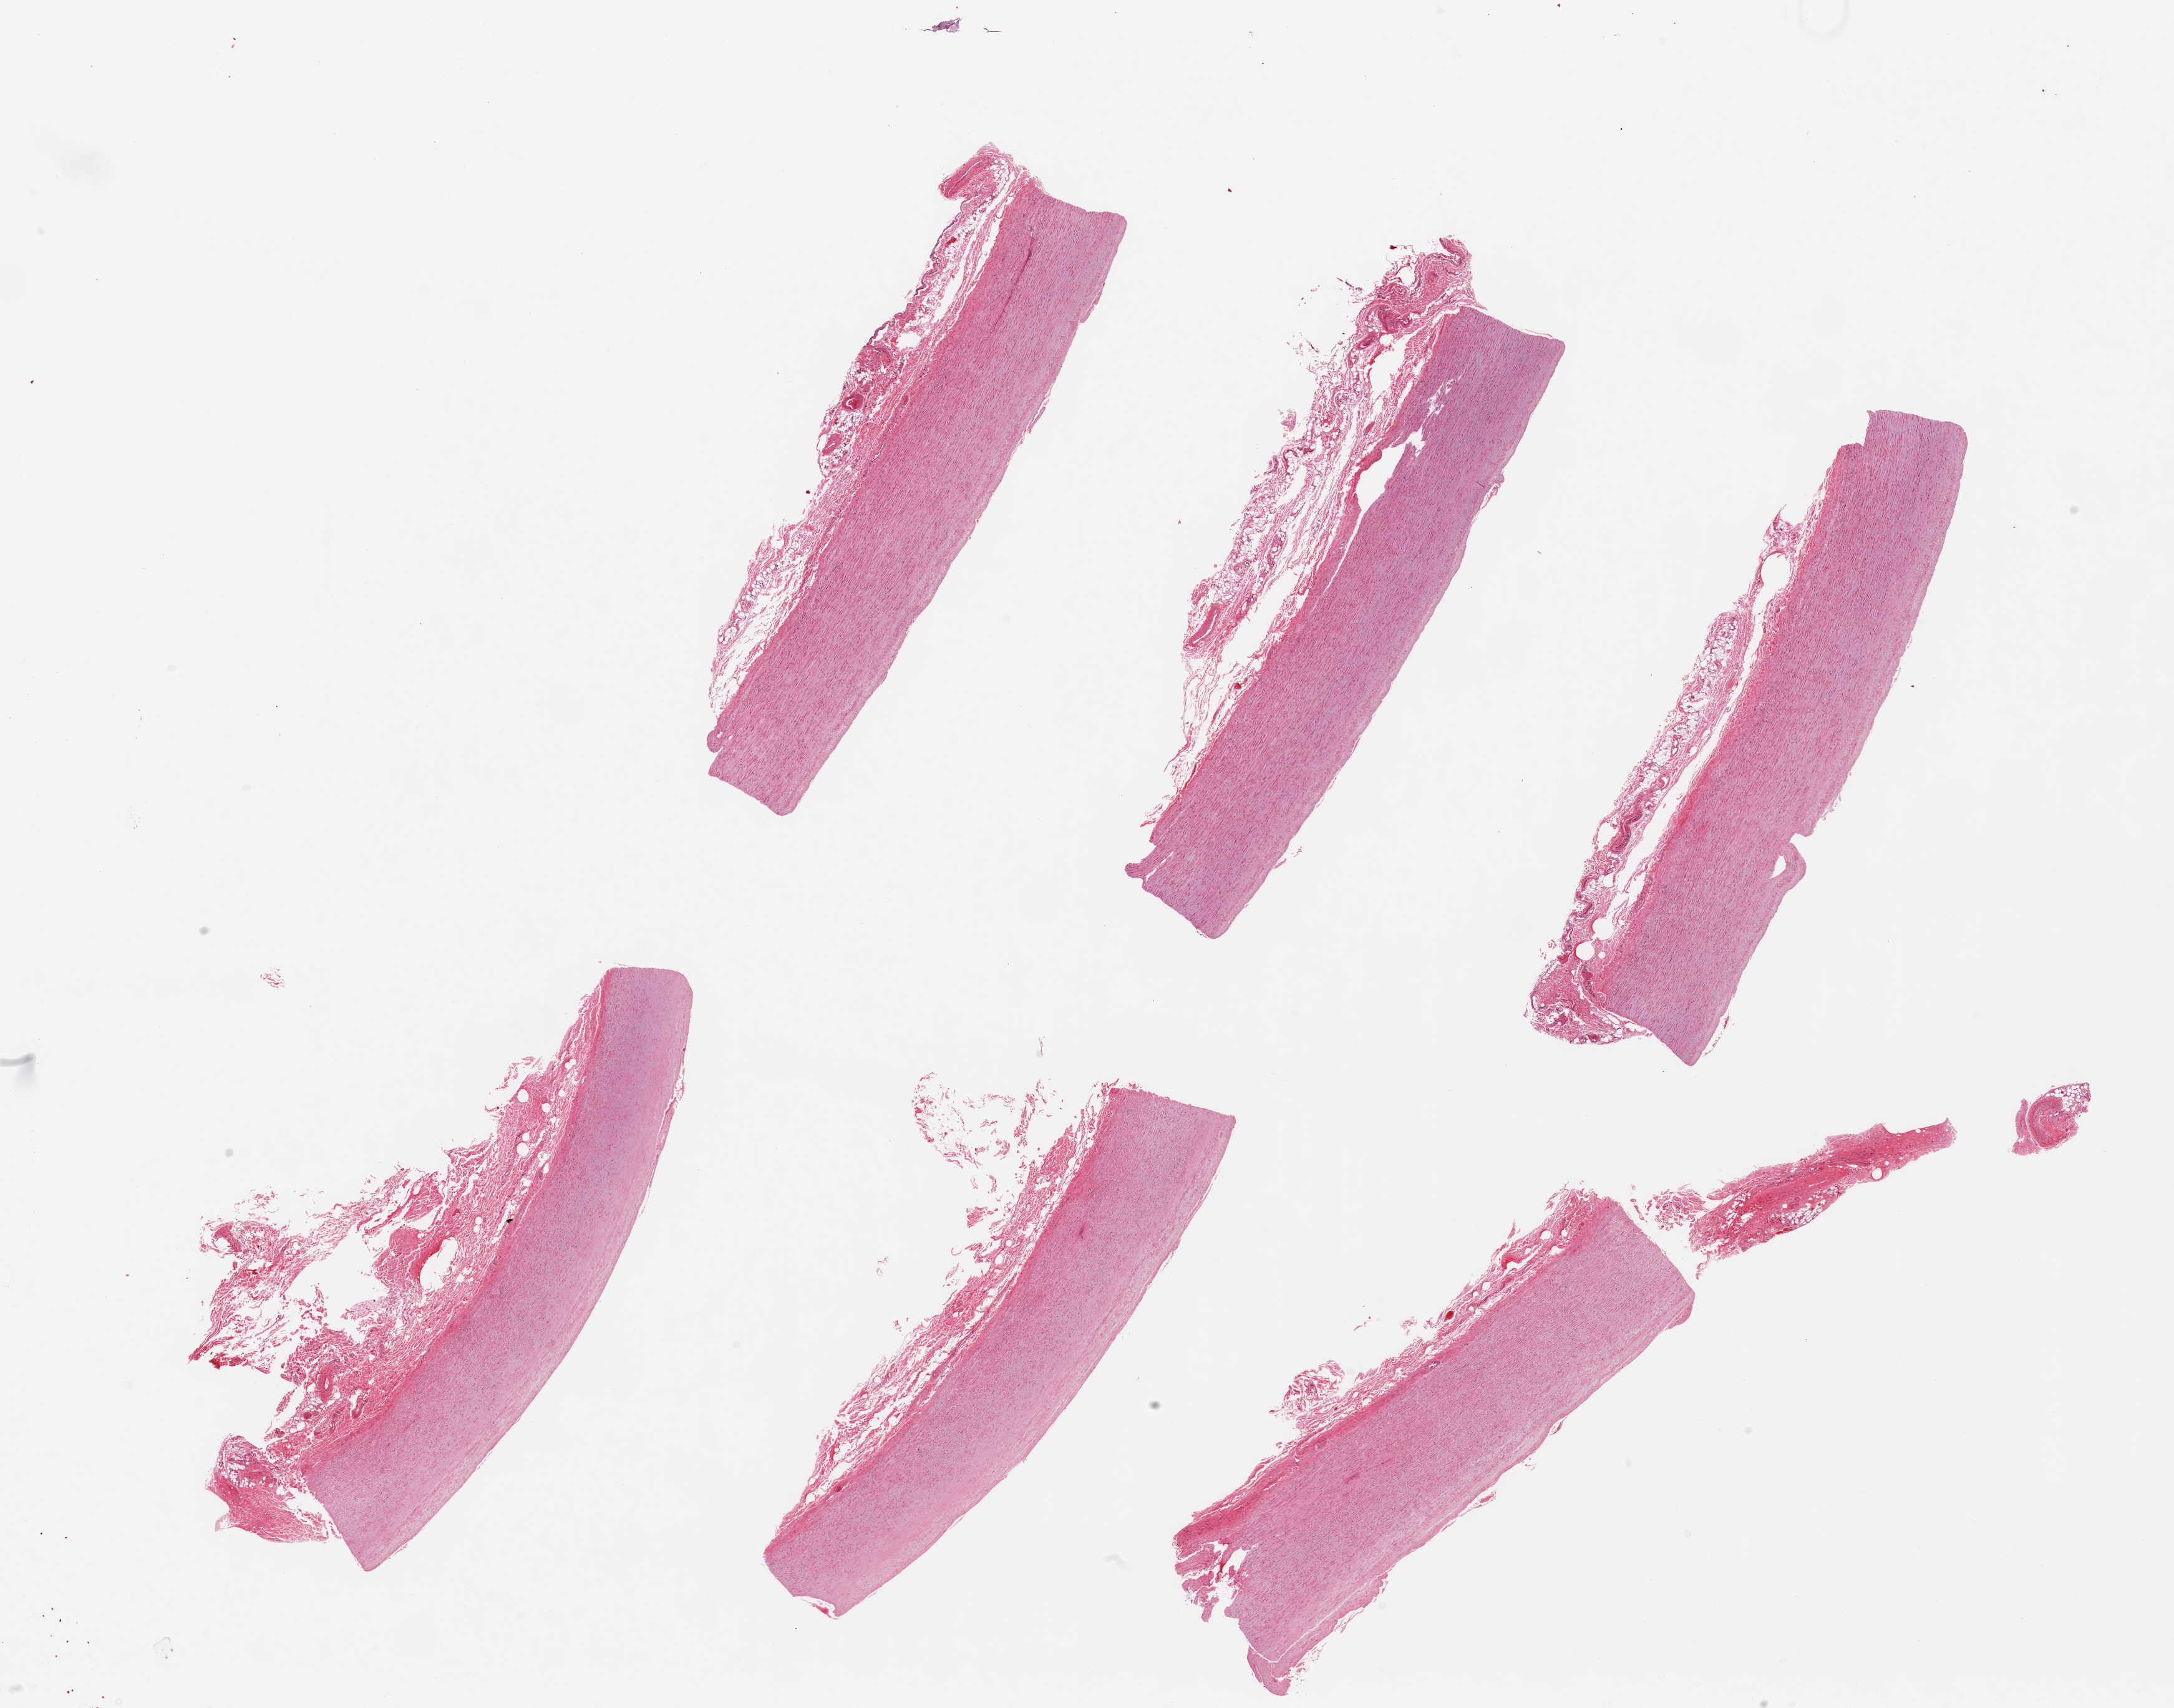
Digitized hematoxylin and eosin (H&E)-stained section, brightfield, shown as a low-resolution overview of the whole scanned area (about 27.6 x 21.7 mm); PAXgene-fixed, paraffin-embedded tissue; target tissue: aorta; donor tissue sample. Donor sex: female.
Review note (as recorded): 6 ~8.5x1.5mm pieces, some with 0.5-1mm attached fibroadipose tissue on serosal surfaces.